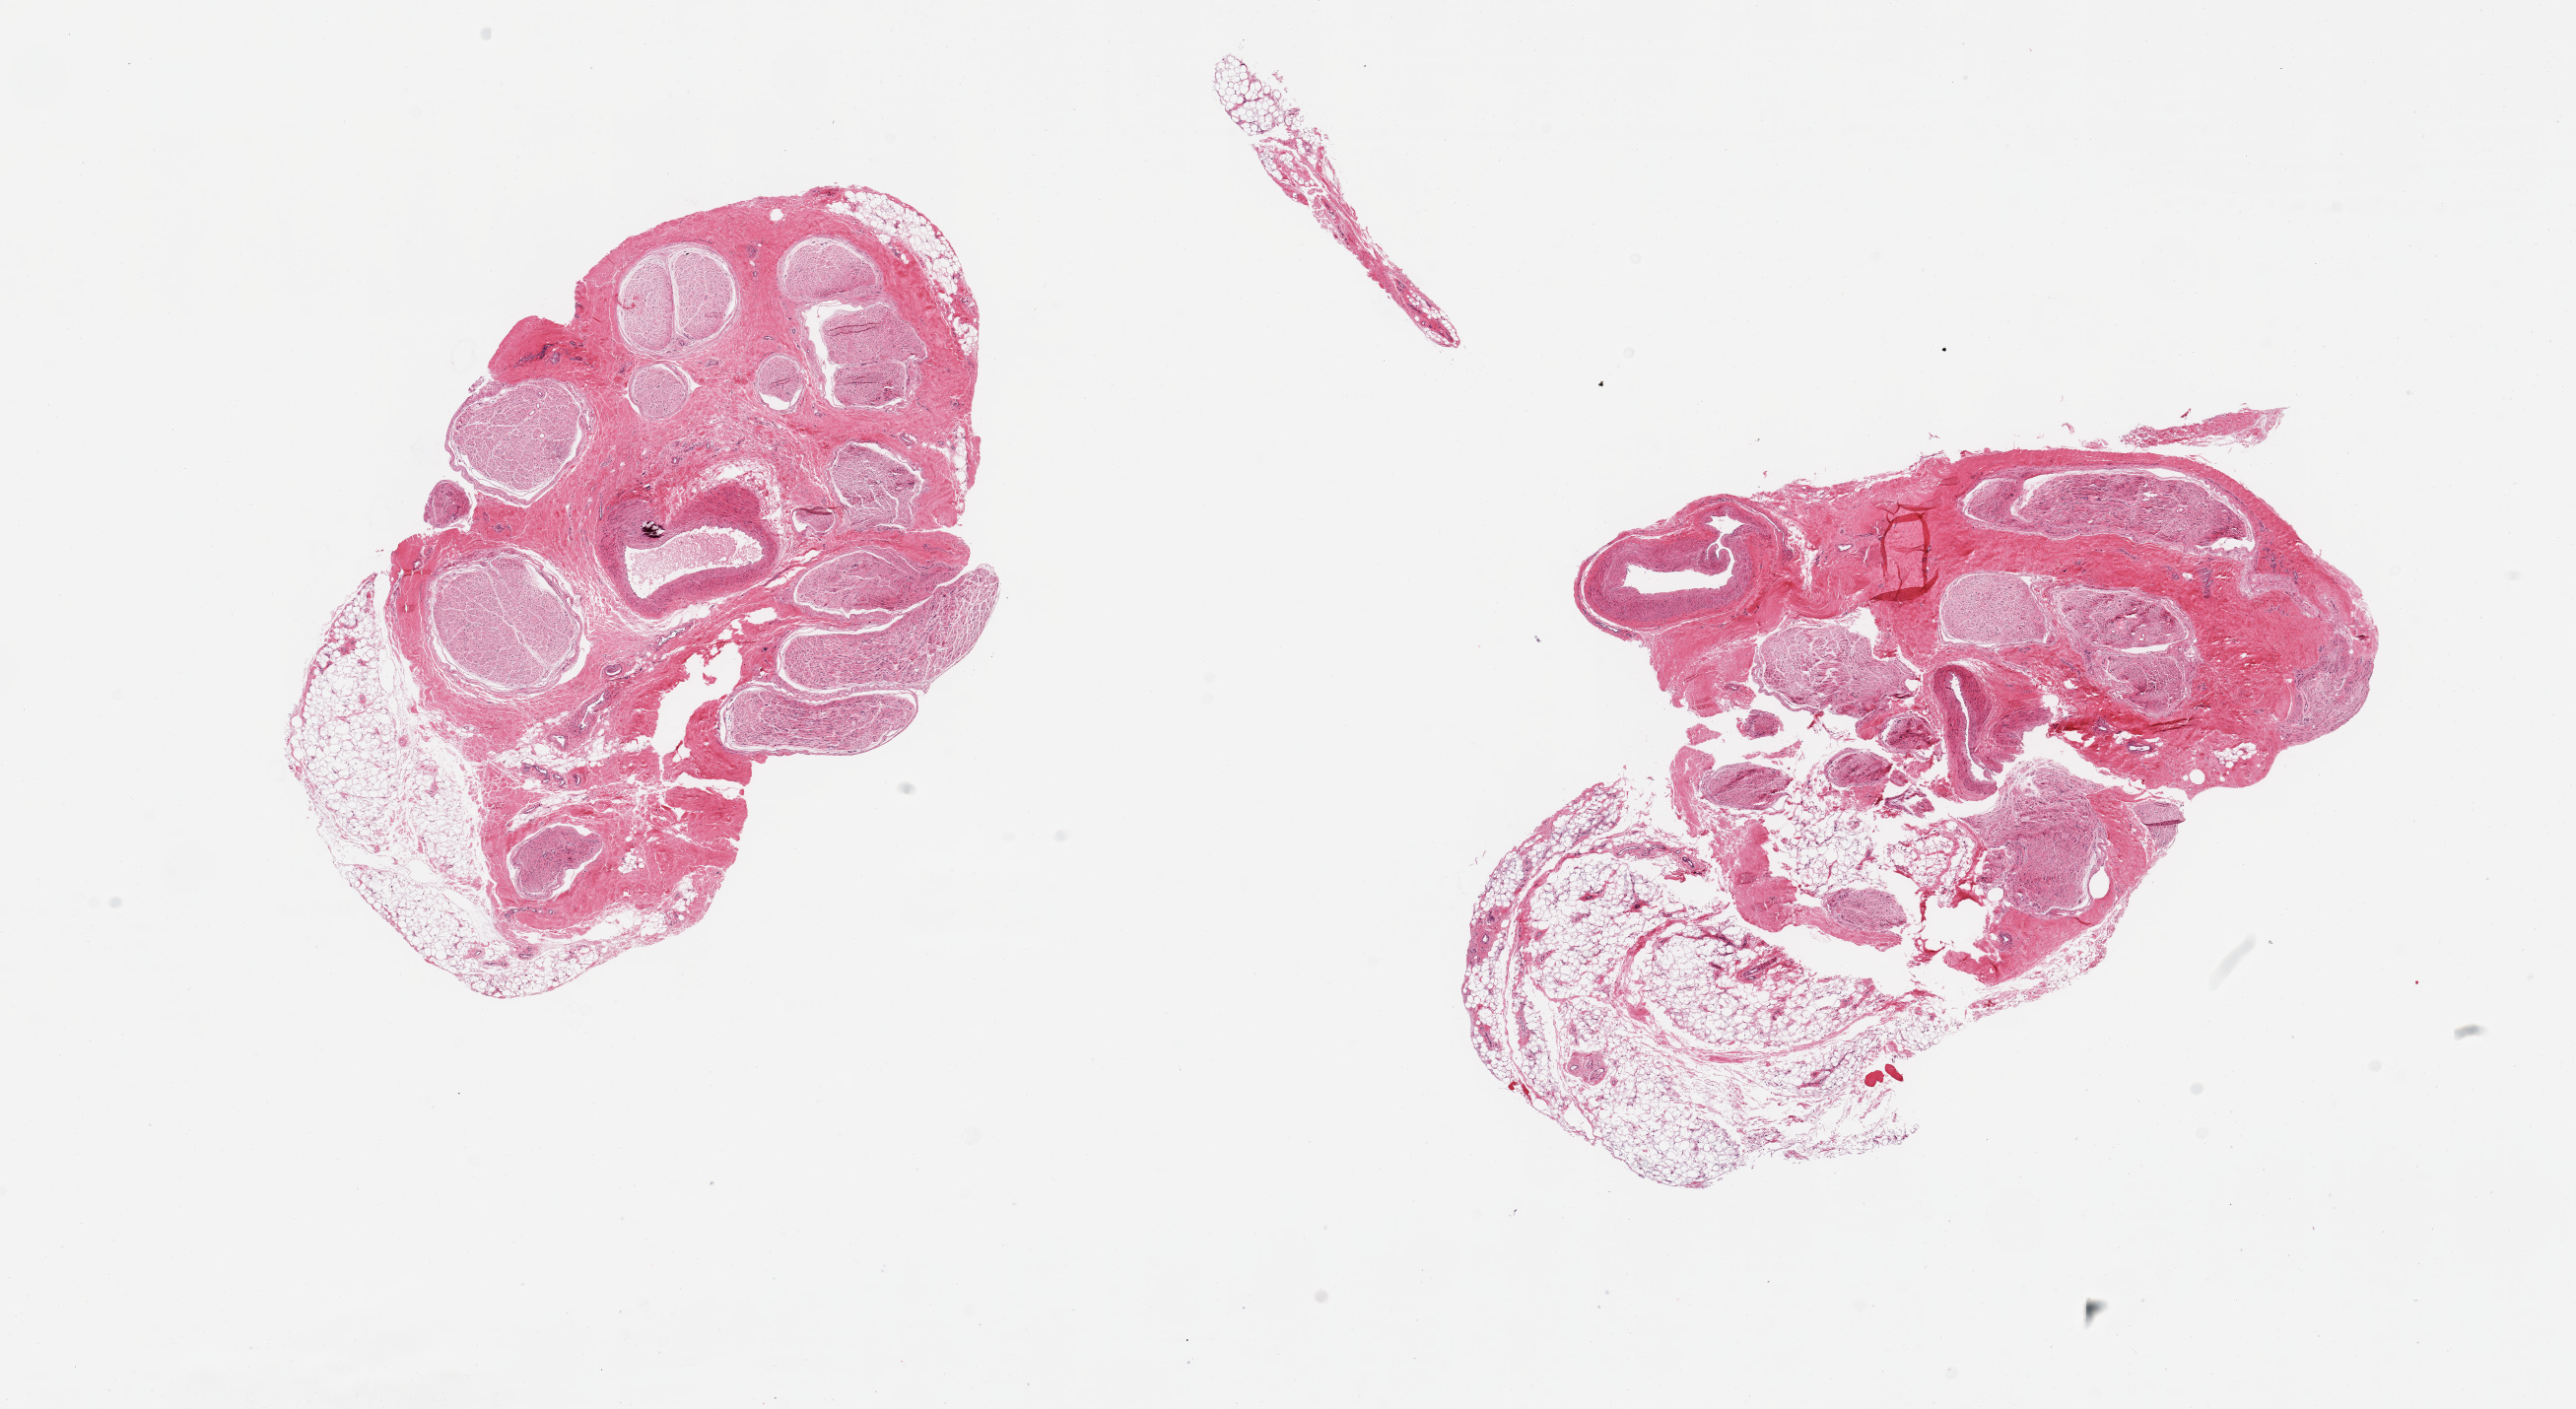
Digitized haematoxylin and eosin-stained section, whole scanned area (about 20.7 x 11.3 mm) shown as a low-resolution overview, PAXgene-fixed paraffin-embedded (PFPE) section, section of tibial nerve (target tissue), tissue donor sample. Donor: male.
Pathologist's review note for this sample: 2 pieces; 30 and 60% fibrofatty content.